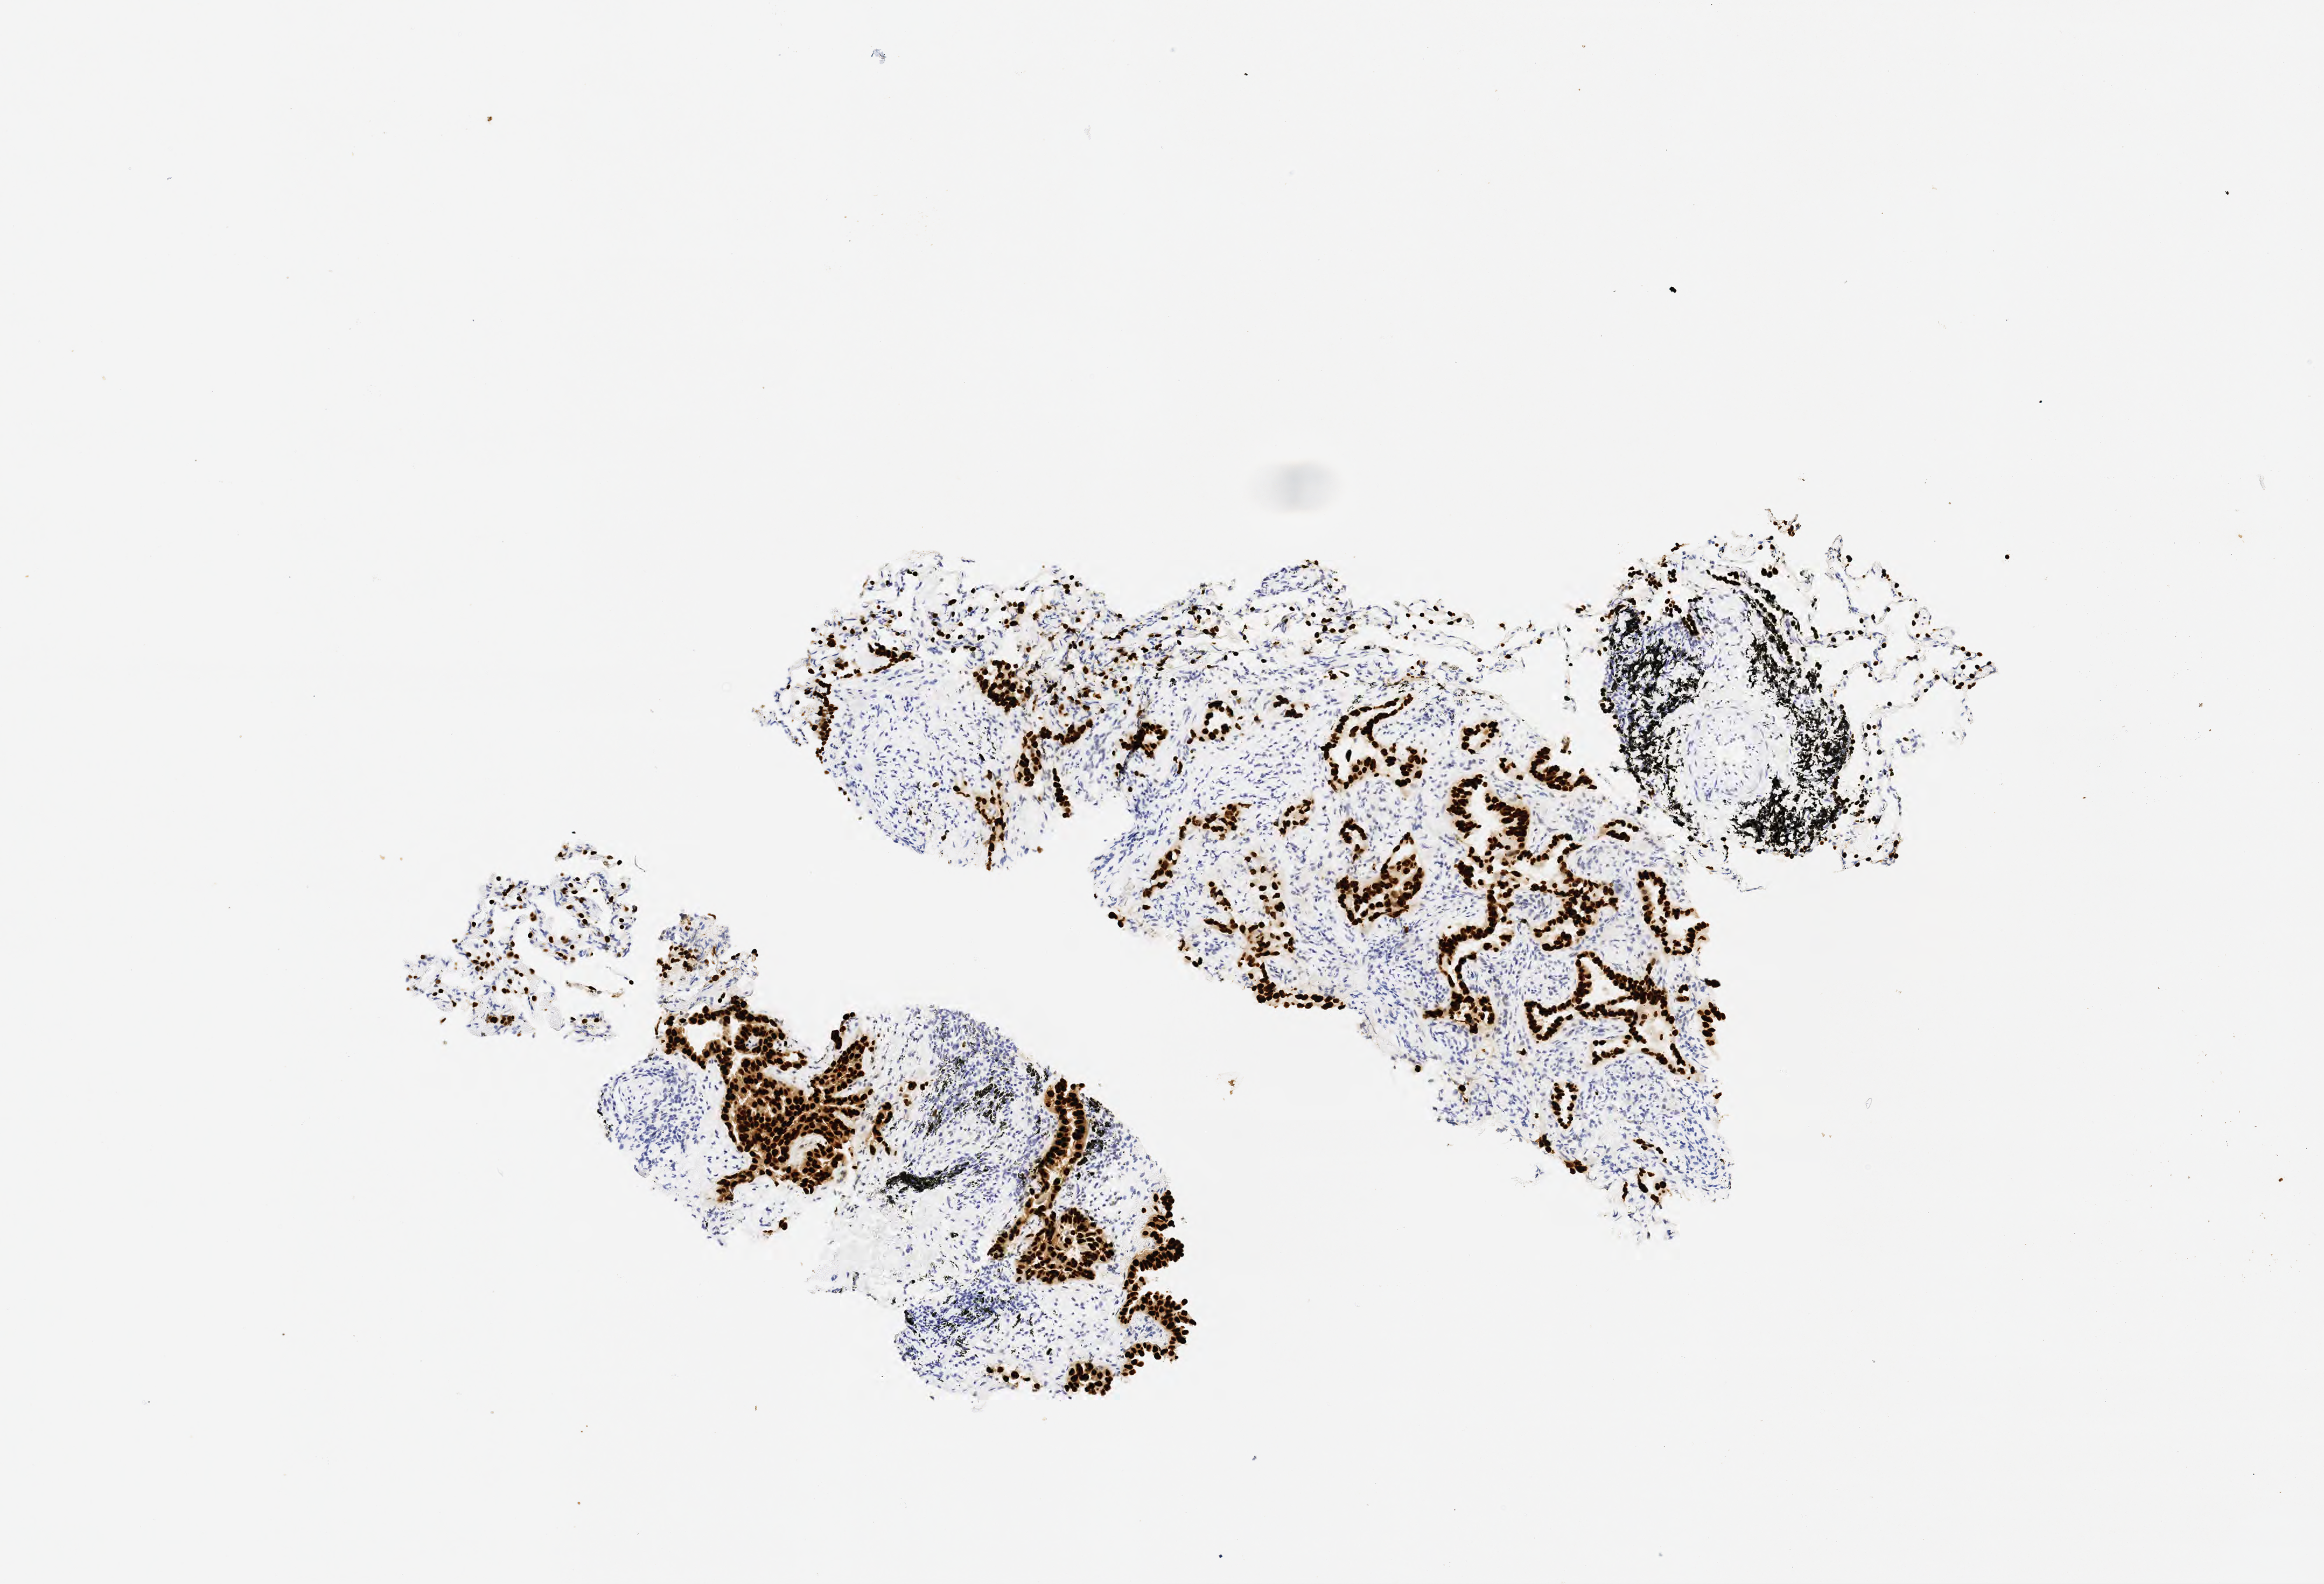
Immunohistochemistry (IHC) whole-slide image stained for TTF-1 (thyroid transcription factor 1), whole scanned area (about 4.0 x 2.7 mm) shown as a low-resolution overview; specimen: tumor tissue; site: lung. Patient: female, 63 years old.
* diagnosis: Adenocarcinoma, NOS